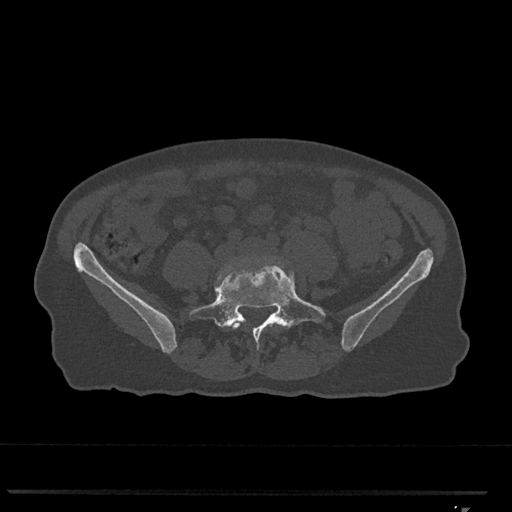
CT including the spine, one axial slice. Position 165 of 793 along the scan axis. Reconstruction kernel Br40s/3. Bone window (W 1800 / L 400 HU). 0.5 mm slice thickness. 512 × 512 image matrix, field of view 380 × 380 mm. Female patient, age 62 years. From the clinical record (not read from this slice): primary cancer: renal.
Outlined on this slice (semi-automatically segmented with operator editing):
- L4 vertebra: bounding box [x1, y1, x2, y2] px = [217, 258, 257, 329]
- L5 vertebra: [189, 261, 326, 349]